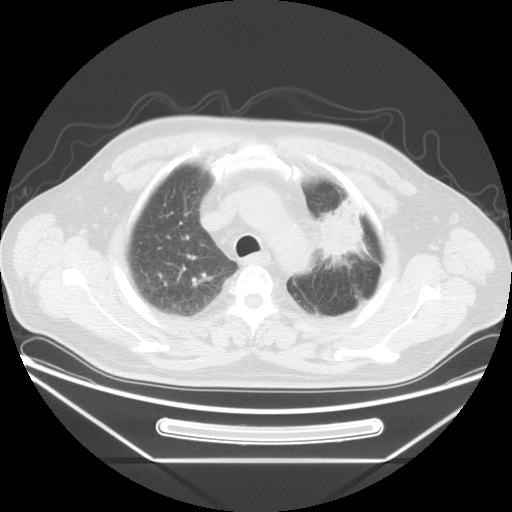
Chest CT, one axial slice. Slice 31 of 38 in the series (ordered by position). 120 kVp. Lung window (W 1500 / L -600 HU). 5 mm slice thickness. 512 × 512 image matrix, field of view 411 × 411 mm. Male patient, age 61 years. From the clinical record (not read from this slice): clinical TNM (as recorded): T2a N0 M0.
Outlined on this slice (bounding box drawn by a radiologist):
- lung tumour (recorded histology: small cell carcinoma): bounding box [x1, y1, x2, y2] px = [310, 192, 375, 264]